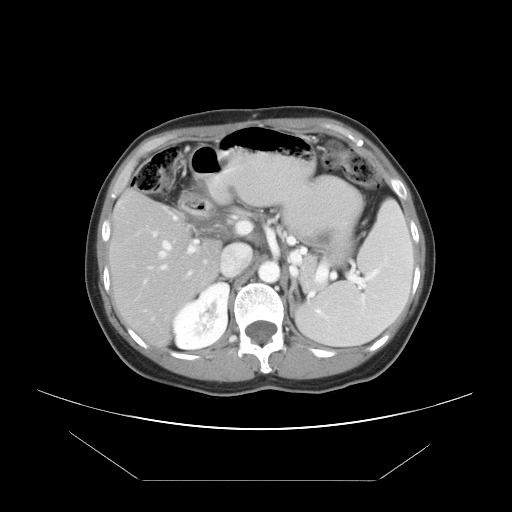
Contrast-enhanced abdominal CT, one axial slice. Position 27 of 45 along the scan axis. Reconstruction kernel STANDARD. 120 kVp. Intravenous contrast given. Soft-tissue window (W 400 / L 40 HU). 5 mm slice thickness. 512 × 512 image matrix. Female patient, age 52 years. Case-level facts recorded for this patient, not image findings: diagnosis: colorectal cancer liver metastases, imaged before liver resection; multiple liver metastases: yes.
Outlined on this slice (outlined manually by an expert reader):
- hepatic veins: bounding box (x1, y1, x2, y2) in pixels: (160, 241, 171, 269)
- liver: (113, 194, 221, 342)
- planned liver remnant (the part of the liver to remain after resection): (113, 194, 221, 342)
- portal vein (with intrahepatic branches): (152, 215, 199, 276)